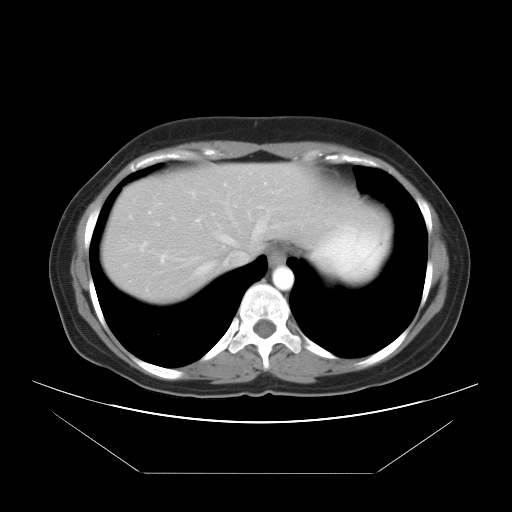
Contrast-enhanced abdominal CT, one axial slice. Position 31 of 34 along the scan axis. 120 kVp. Intravenous contrast given. Soft-tissue window (W 400 / L 40 HU). 7.5 mm slice thickness. 512 × 512 image matrix, field of view 410 × 410 mm. Female patient, age 38 years. Case-level facts recorded for this patient, not image findings: diagnosis: colorectal cancer liver metastases, imaged before liver resection; multiple liver metastases: yes; largest metastasis: 3.1 cm; disease in both lobes: no.
Outlined on this slice (outlined manually by an expert reader):
- hepatic veins: box from (x=194, y=218) to (x=265, y=276) px
- liver: (x=101, y=163)–(x=351, y=303)
- planned liver remnant (the part of the liver to remain after resection): (x=201, y=163)–(x=350, y=257)
- portal vein (with intrahepatic branches): (x=213, y=187)–(x=271, y=219)